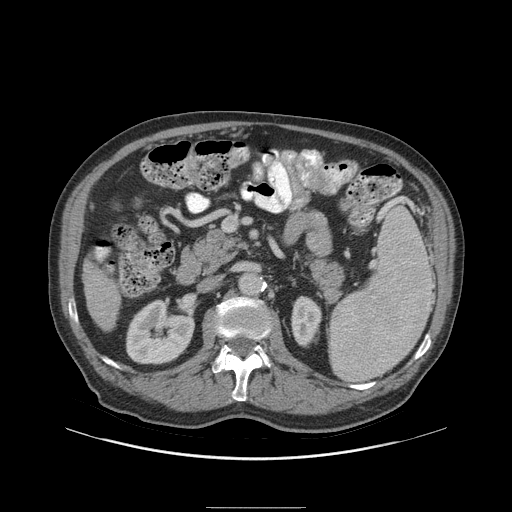
Contrast-enhanced abdominal CT (liver protocol), one axial slice; position 31 of 105 along the scan axis; soft-tissue window (W 400 / L 40 HU); 2.5 mm slice thickness; 512 × 512 image matrix, field of view 440 × 440 mm. Case-level facts recorded for this patient, not image findings: diagnosis: hepatocellular carcinoma (patient treated with transarterial chemoembolisation; whether this scan precedes or follows treatment is not stated here); TNM stage (as recorded): Stage-I; Child-Pugh class: A; tumour size: 5.1 cm.
Outlined on this slice (semi-automatic segmentation, software-assisted and operator-edited):
- liver parenchyma outside the tumour (the mass and vessels are separate outlines, so this box may not span the whole liver): bounding box <82,258,120,330> (left, top, right, bottom; pixels)